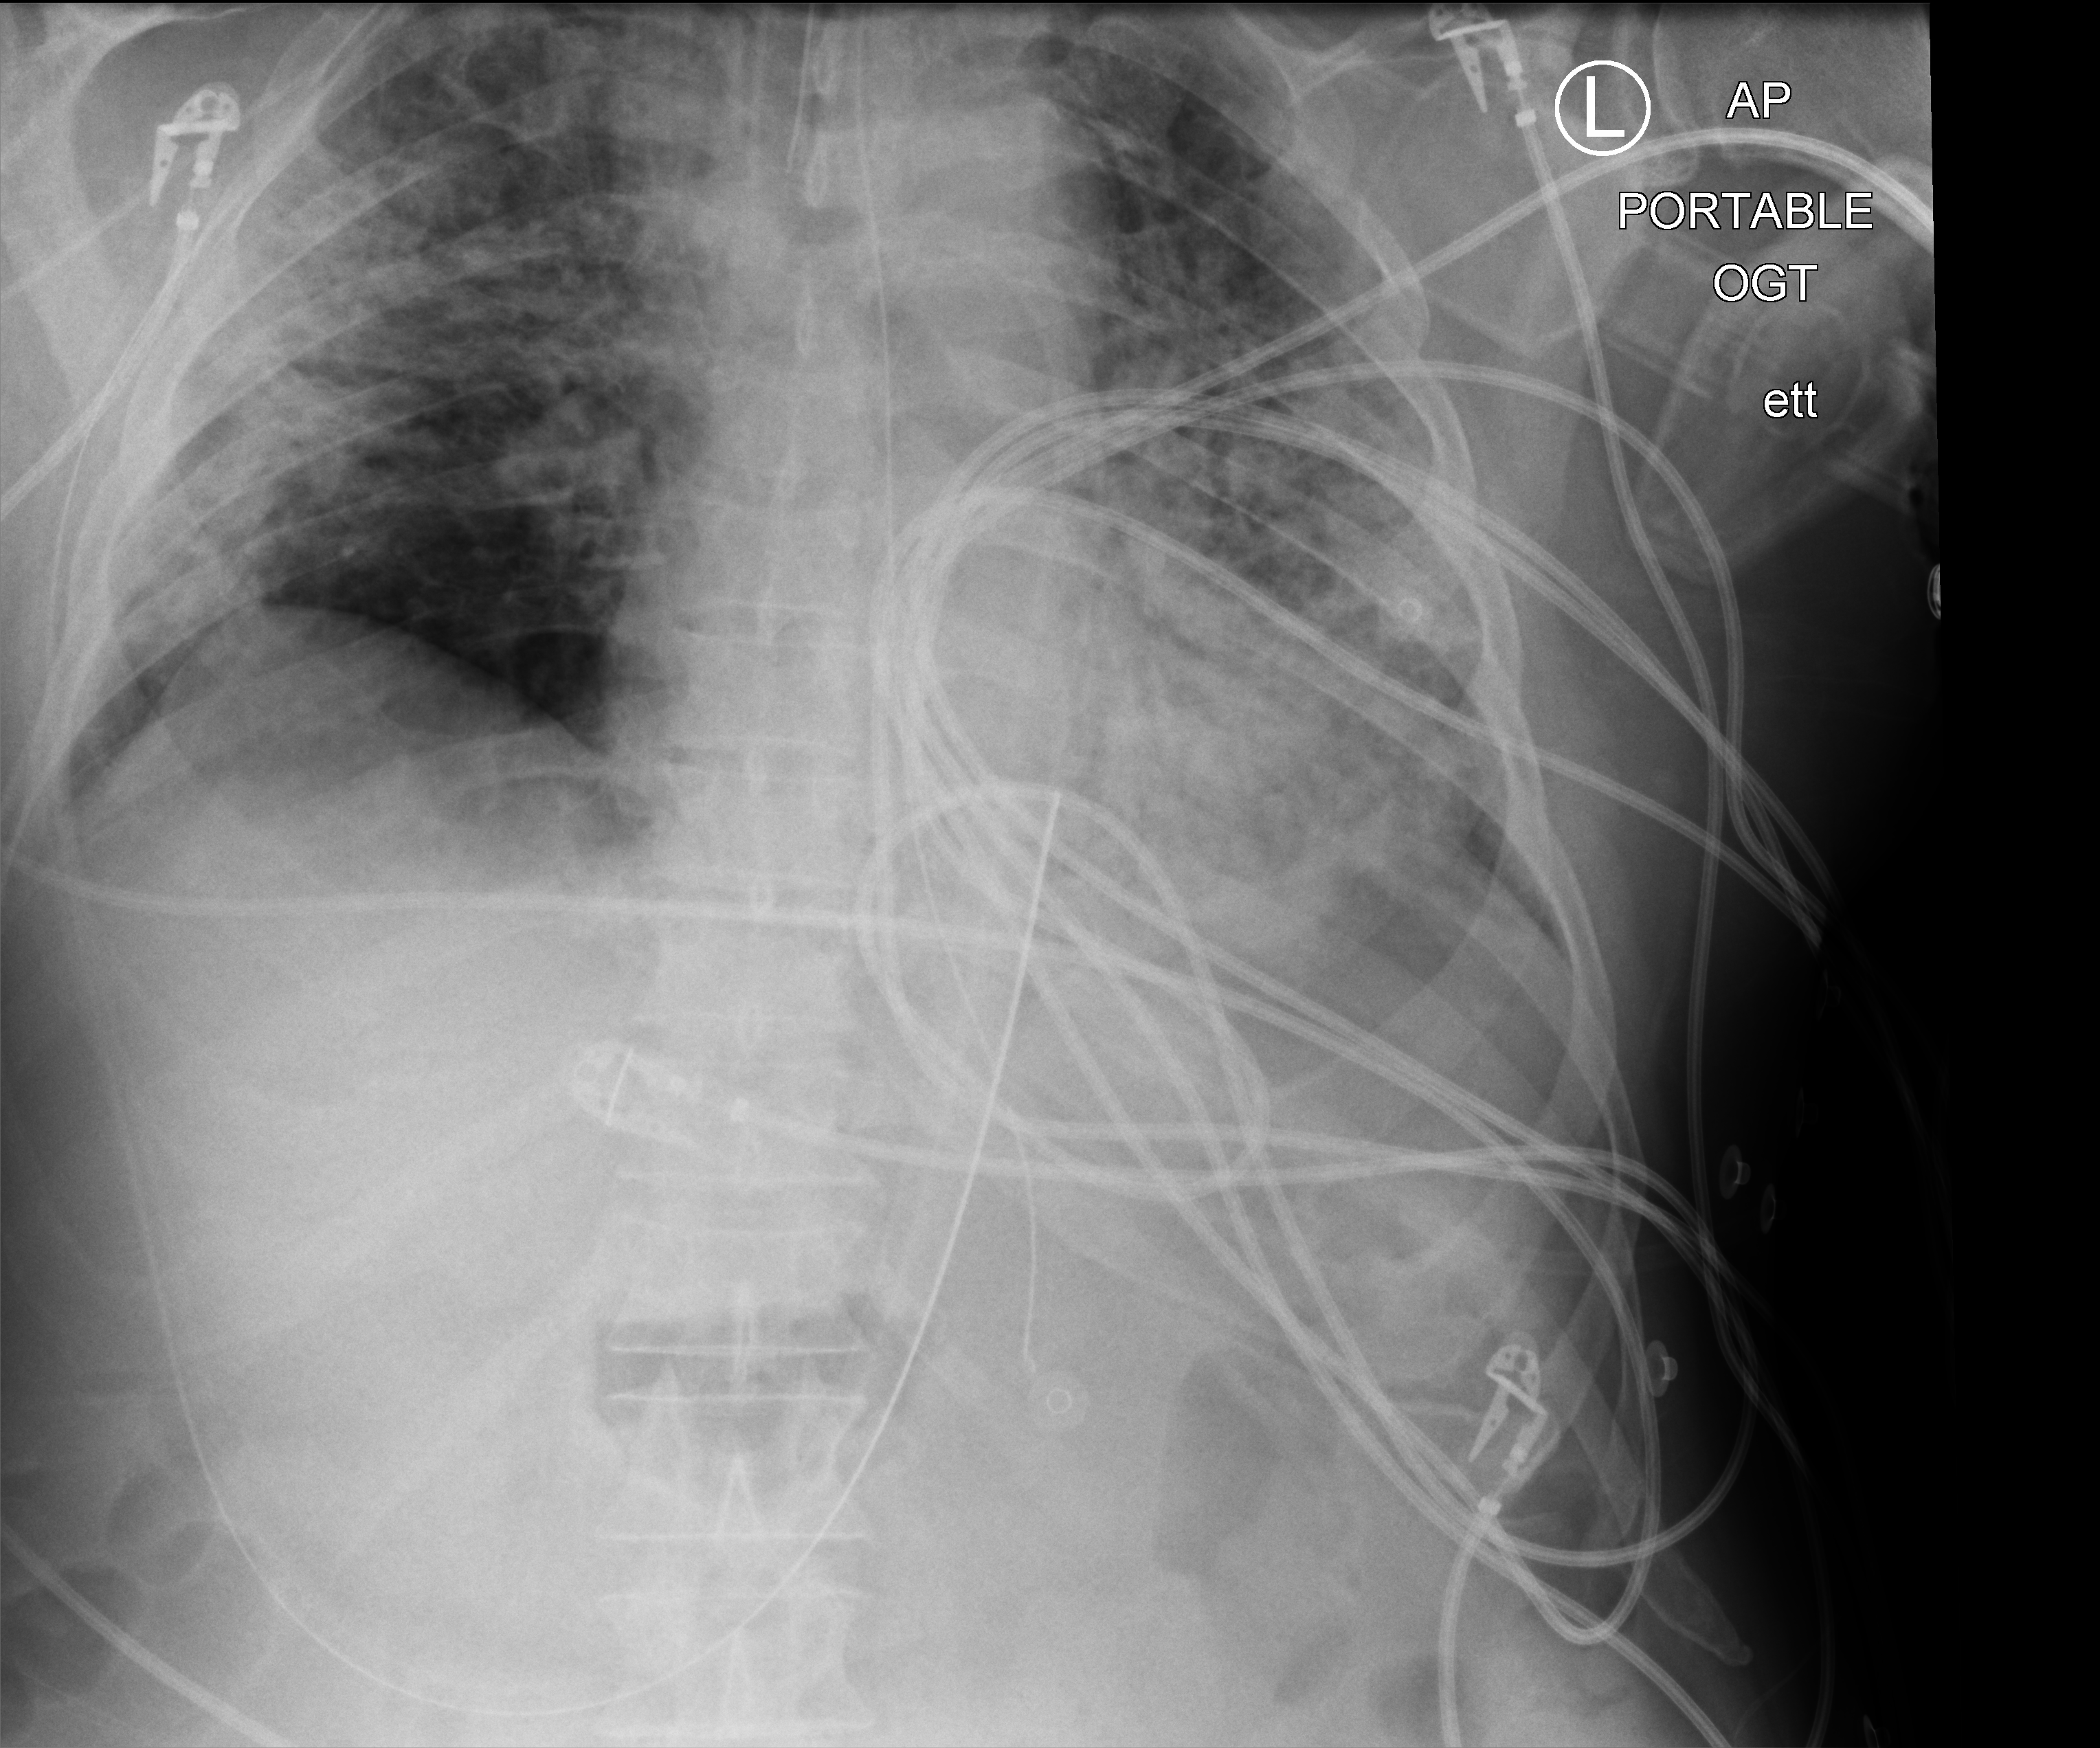
Bedside chest radiograph (computed radiography). Male patient hospitalised with COVID-19, age 60–74 years.
From the hospital-stay record, not from the radiograph (when in the stay this image was taken is not recorded):
- admitted to intensive care during this hospital stay: yes
- diabetes (admission record): yes